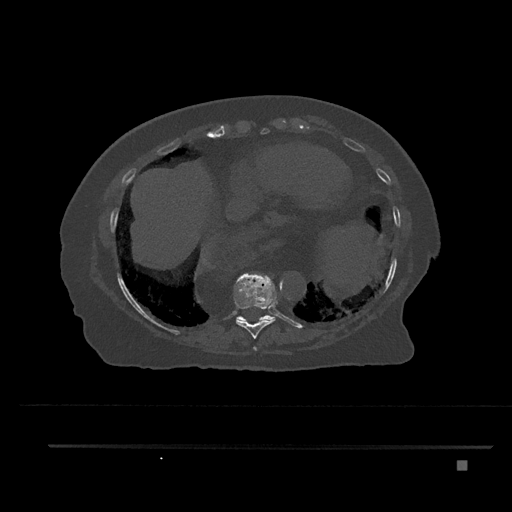
CT including the spine, one axial slice. Slice 387 of 797 in the series (ordered by position). Reconstruction kernel Br40s/3. 120 kVp. Bone window (W 1800 / L 400 HU). 0.5 mm slice thickness. 512 × 512 image matrix, field of view 437 × 437 mm. Patient: female, 76 years. From the clinical record (not read from this slice): primary cancer: lung; vertebrae with lytic lesions (as recorded): T11, L3.
Outlined on this slice (semi-automatically segmented with operator editing):
- T10 vertebra: bounding box <236,315,275,322> (left, top, right, bottom; pixels)
- T8 vertebra: <253,346,257,351>
- T9 vertebra: <234,273,277,339>